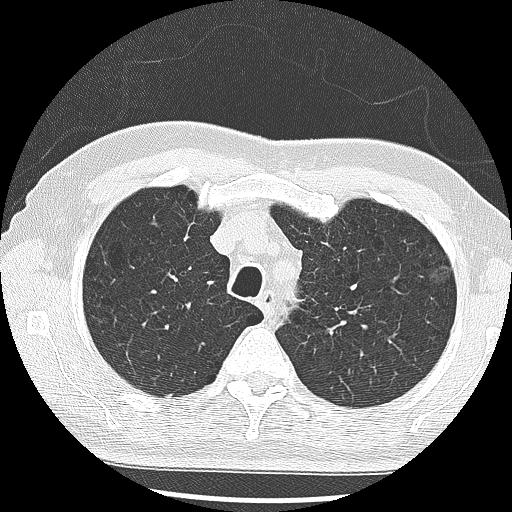
Low-dose screening chest CT, one axial slice. Position 223 of 285 along the scan axis. Reconstruction kernel LUNG. 120 kVp. Lung window (W 1500 / L -600 HU). 2.5 mm slice thickness. 512 × 512 image matrix, field of view 340 × 340 mm.
Structures marked on this image (expert manual segmentation):
- lesion 1 (tumor, upper lobe of left lung): bounding box <431,266,451,281> (left, top, right, bottom; pixels)